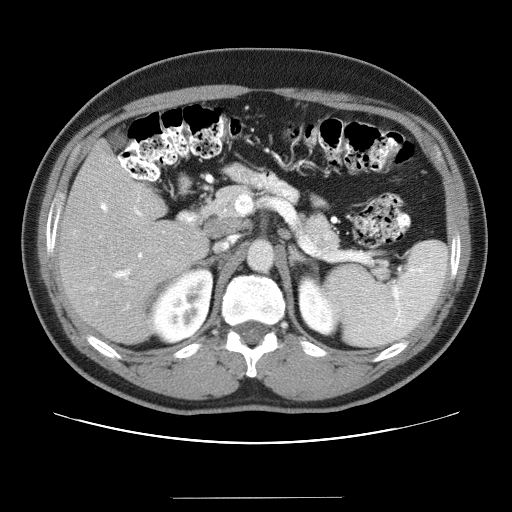
Contrast-enhanced abdominal CT (liver protocol), one axial slice; position 16 of 40 along the scan axis; 120 kVp; soft-tissue window (W 400 / L 40 HU); 5 mm slice thickness; 512 × 512 image matrix, field of view 380 × 380 mm. From the clinical record (not read from this slice): diagnosis: hepatocellular carcinoma (patient treated with transarterial chemoembolisation; whether this scan precedes or follows treatment is not stated here); TNM stage (as recorded): Stage-IVA; Child-Pugh class: B.
Annotated regions visible in this slice (semi-automatically segmented with operator editing):
- liver parenchyma outside the tumour (the mass and vessels are separate outlines, so this box may not span the whole liver): bounding box <56,140,208,342> (left, top, right, bottom; pixels)
- liver vessels: <88,173,164,308>